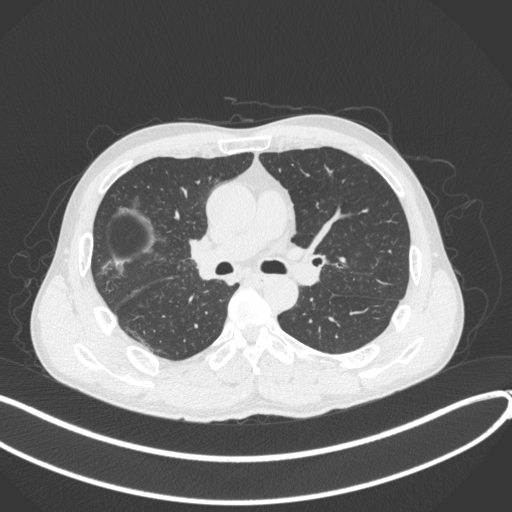
Chest CT, one axial slice. Slice 229 of 409 in the series (ordered by position). Reconstruction kernel B31f. Lung window (W 1500 / L -600 HU). 1 mm slice thickness. 512 × 512 image matrix, field of view 400 × 400 mm. Male patient, age 53 years. From the clinical record (not read from this slice): clinical TNM (as recorded): T1b N0 M0.
Structures marked on this image (bounding box drawn by a radiologist):
- lung tumour (recorded histology: squamous cell carcinoma): bounding box <190,232,226,289> (left, top, right, bottom; pixels)